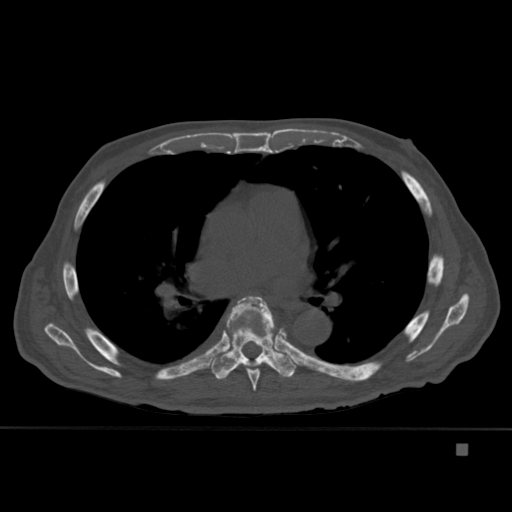
CT including the spine, one axial slice; slice 285 of 451 in the series (ordered by position); bone window (W 1800 / L 400 HU); 1.5 mm slice thickness; 512 × 512 image matrix, field of view 378 × 378 mm. Male patient, age 75 years. Case-level facts recorded for this patient, not image findings: primary cancer: prostate.
Structures marked on this image (semi-automatic segmentation, software-assisted and operator-edited):
- T4 vertebra: bounding box <270,325,285,341> (left, top, right, bottom; pixels)
- T6 vertebra: <236,296,274,391>
- T7 vertebra: <211,297,296,380>